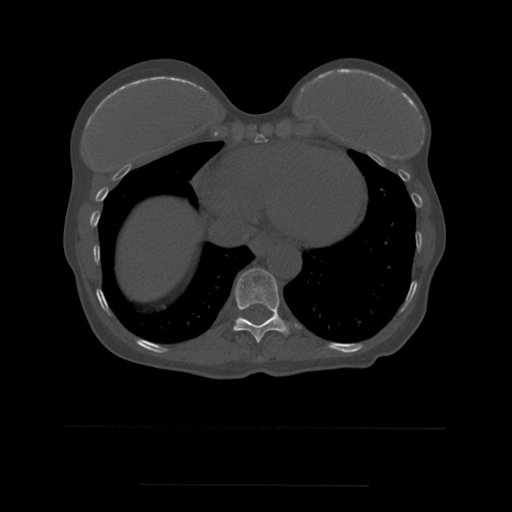
CT including the spine, one axial slice; position 301 of 544 along the scan axis; bone window (W 1800 / L 400 HU); 1.25 mm slice thickness; 512 × 512 image matrix. Patient age 58 years. Case-level facts recorded for this patient, not image findings: primary cancer: lung.
Annotated regions visible in this slice (semi-automatically segmented with operator editing):
- T10 vertebra: bounding box (x1, y1, x2, y2) in pixels: (233, 269, 289, 343)